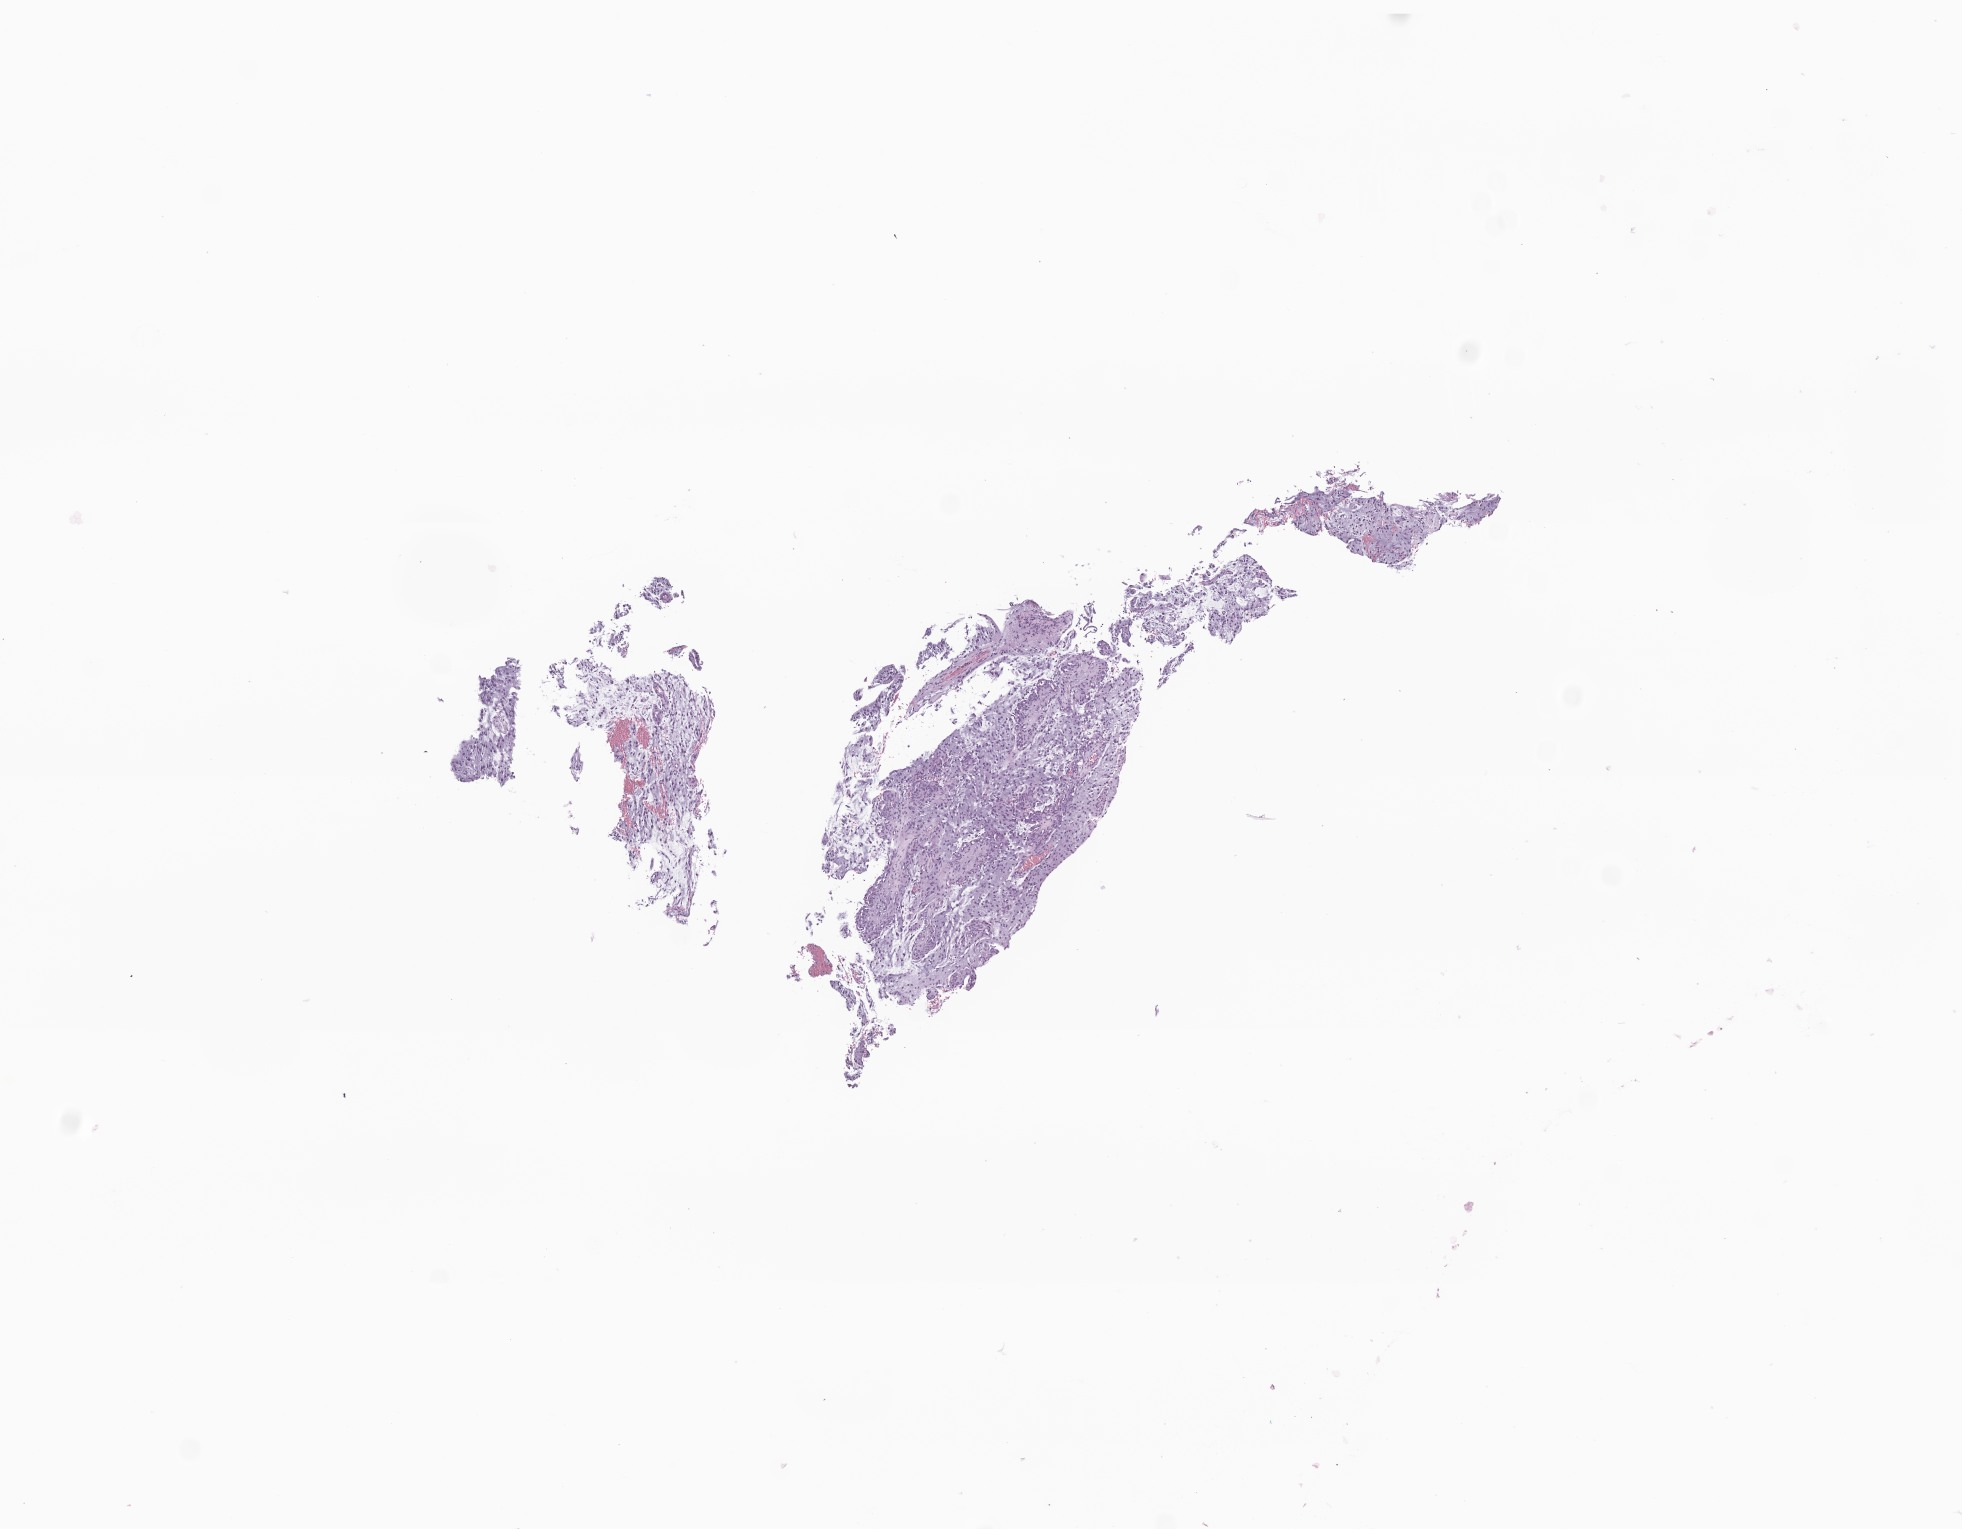
Digitized H&E-stained section of tumor tissue from the brain, shown as a low-resolution overview of the whole scanned area (about 8.3 x 6.4 mm). Formalin-fixed, paraffin-embedded (FFPE) tissue. Male patient, age 120 months (10 years).
* recorded diagnosis: Pilocytic astrocytoma